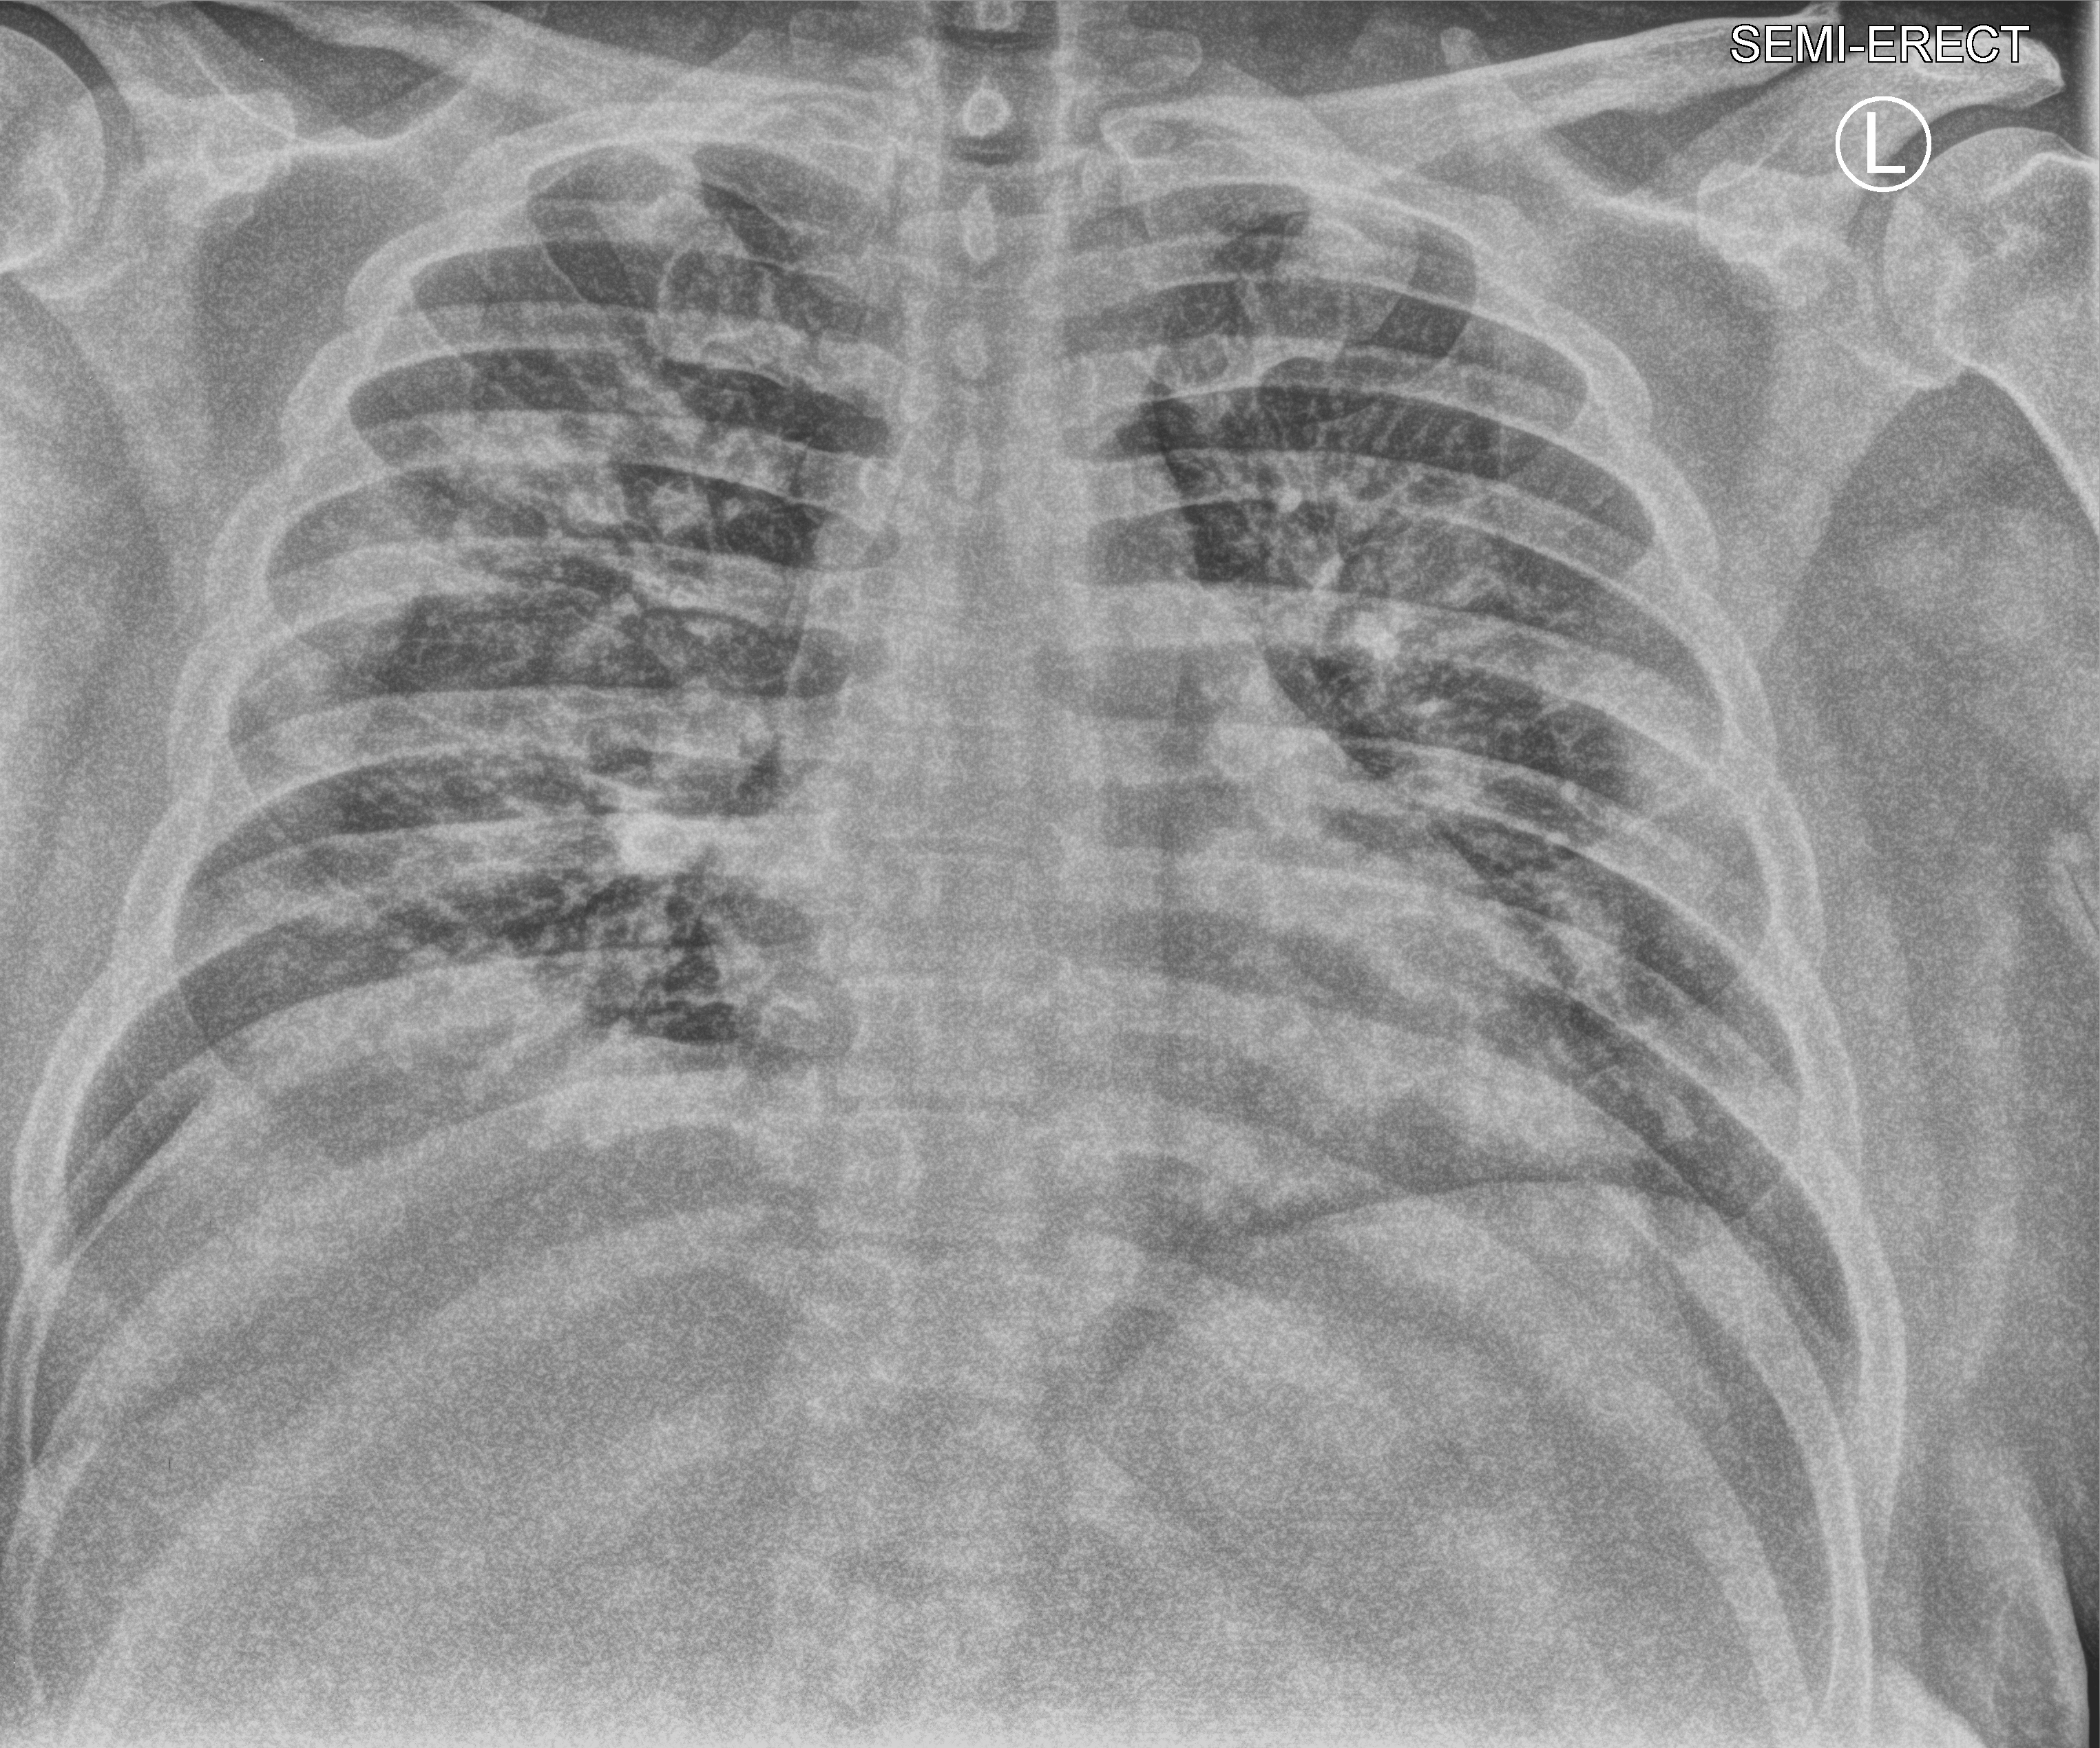
Bedside chest radiograph (computed radiography); anteroposterior (AP) projection. Patient hospitalised with COVID-19; male, aged 18–59 years.
From the hospital-stay record, not from the radiograph (when in the stay this image was taken is not recorded):
- admitted to intensive care during this hospital stay: no